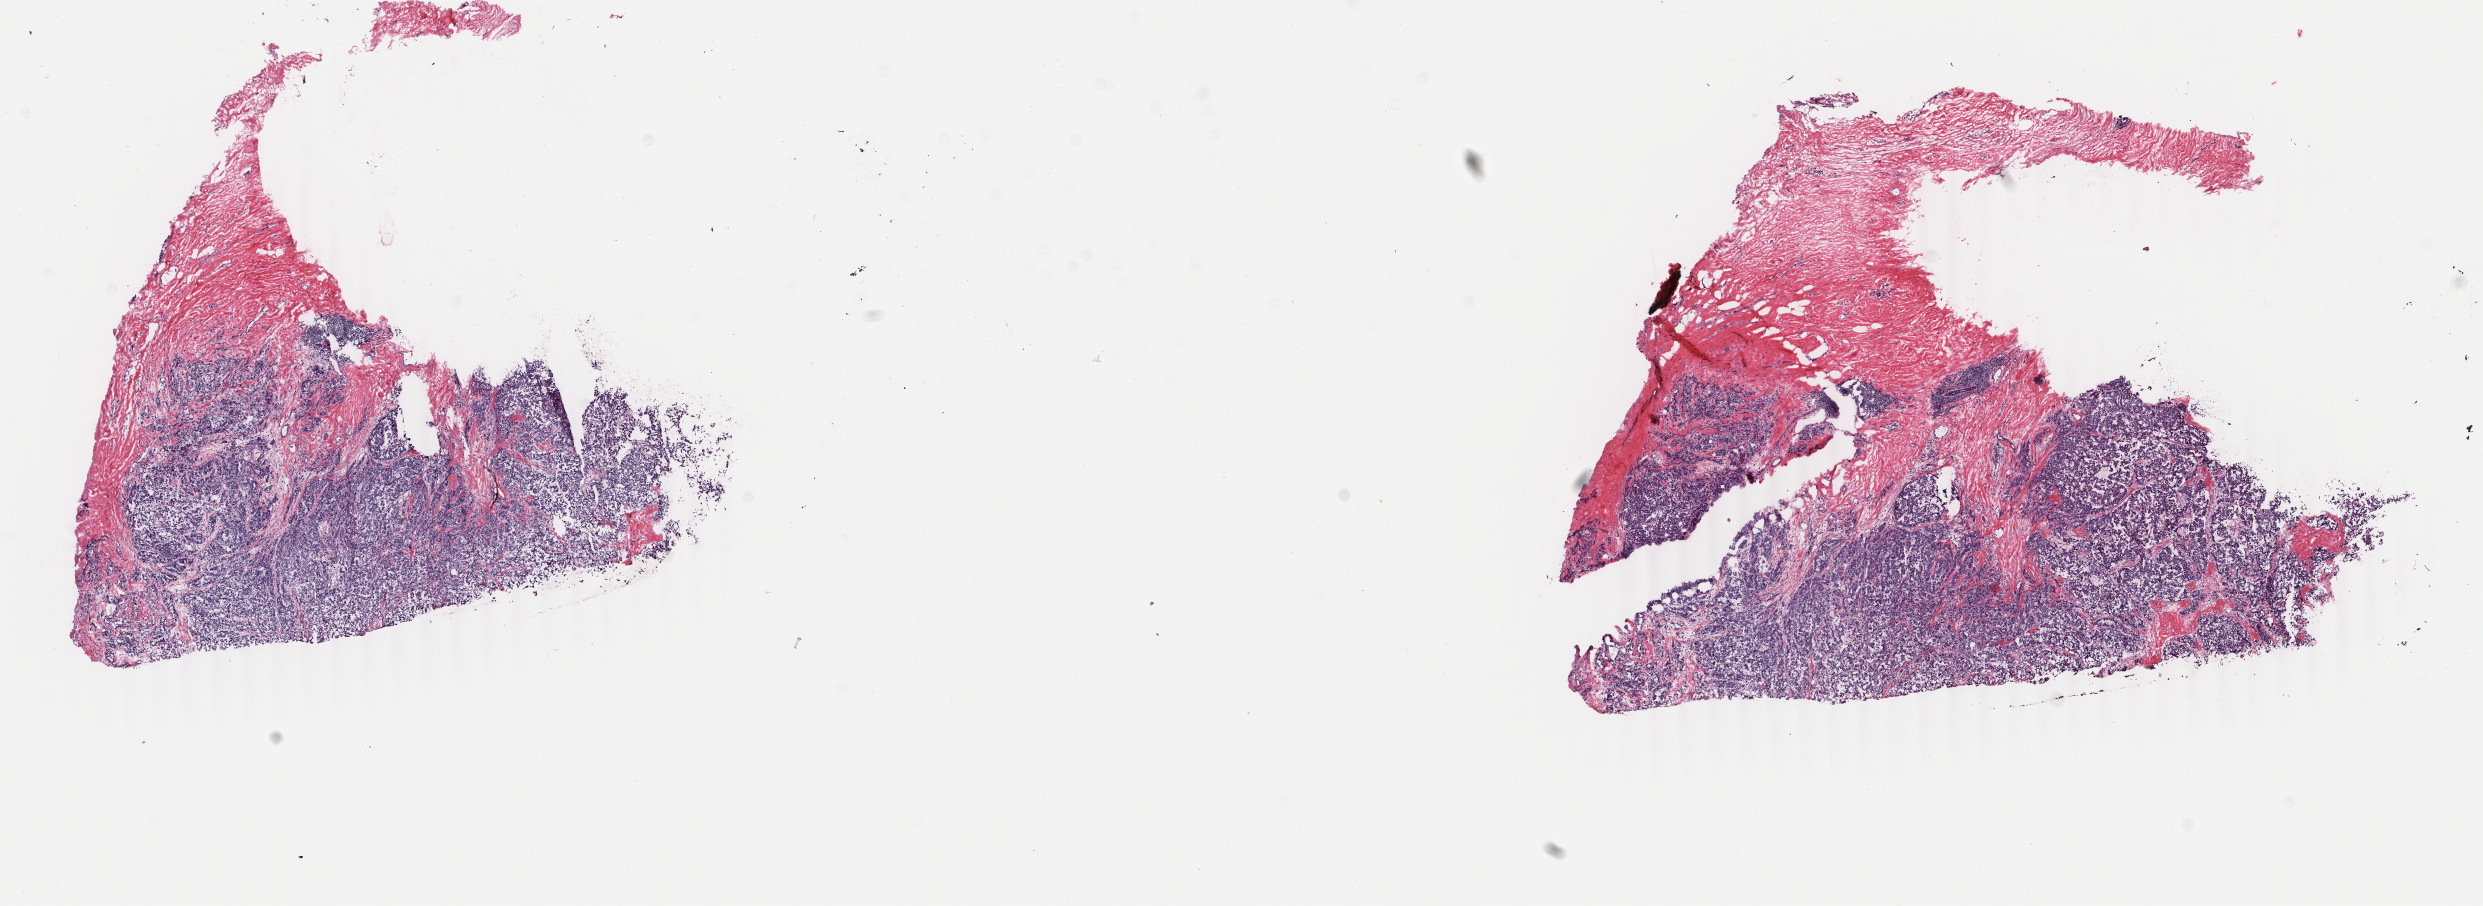
Hematoxylin and eosin (H&E) stained whole-slide image, shown as a low-resolution overview of the whole scanned area (about 19.8 x 7.2 mm, acquisition: 40x scan); frozen section from the top of the tissue portion; primary tumour sample from the breast. Patient: female, age at initial diagnosis 54 years. Slide review estimates, as recorded: tumour cells 75%, tumour nuclei 75%, normal cells 3%, stromal cells 21%, necrosis 1%. Inflammatory infiltration, as recorded: lymphocyte infiltration 2%, monocyte infiltration 0%, neutrophil infiltration 0%.
AJCC pathologic stage: IIA. Laterality: right. Diagnosis: Infiltrating duct carcinoma, NOS.